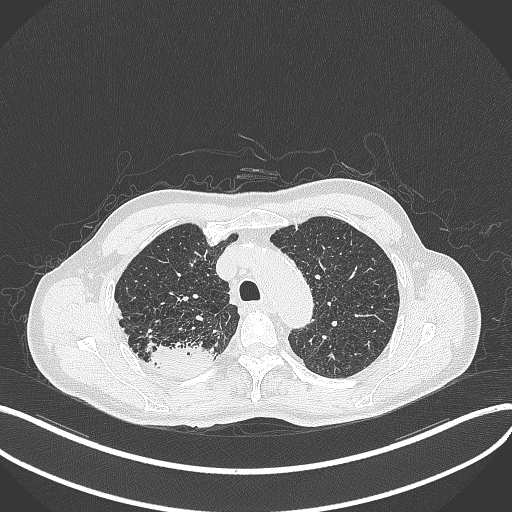
Chest CT, one axial slice; slice 341 of 428 in the series (ordered by position); lung window (W 1500 / L -600 HU); 1 mm slice thickness; 512 × 512 image matrix, field of view 400 × 400 mm. Patient: male, 79 years. From the clinical record (not read from this slice): clinical TNM (as recorded): T3 N0 M0.
Outlined on this slice (bounding box drawn by a radiologist):
- lung tumour (recorded histology: adenocarcinoma): bounding box <143,342,216,379> (left, top, right, bottom; pixels)